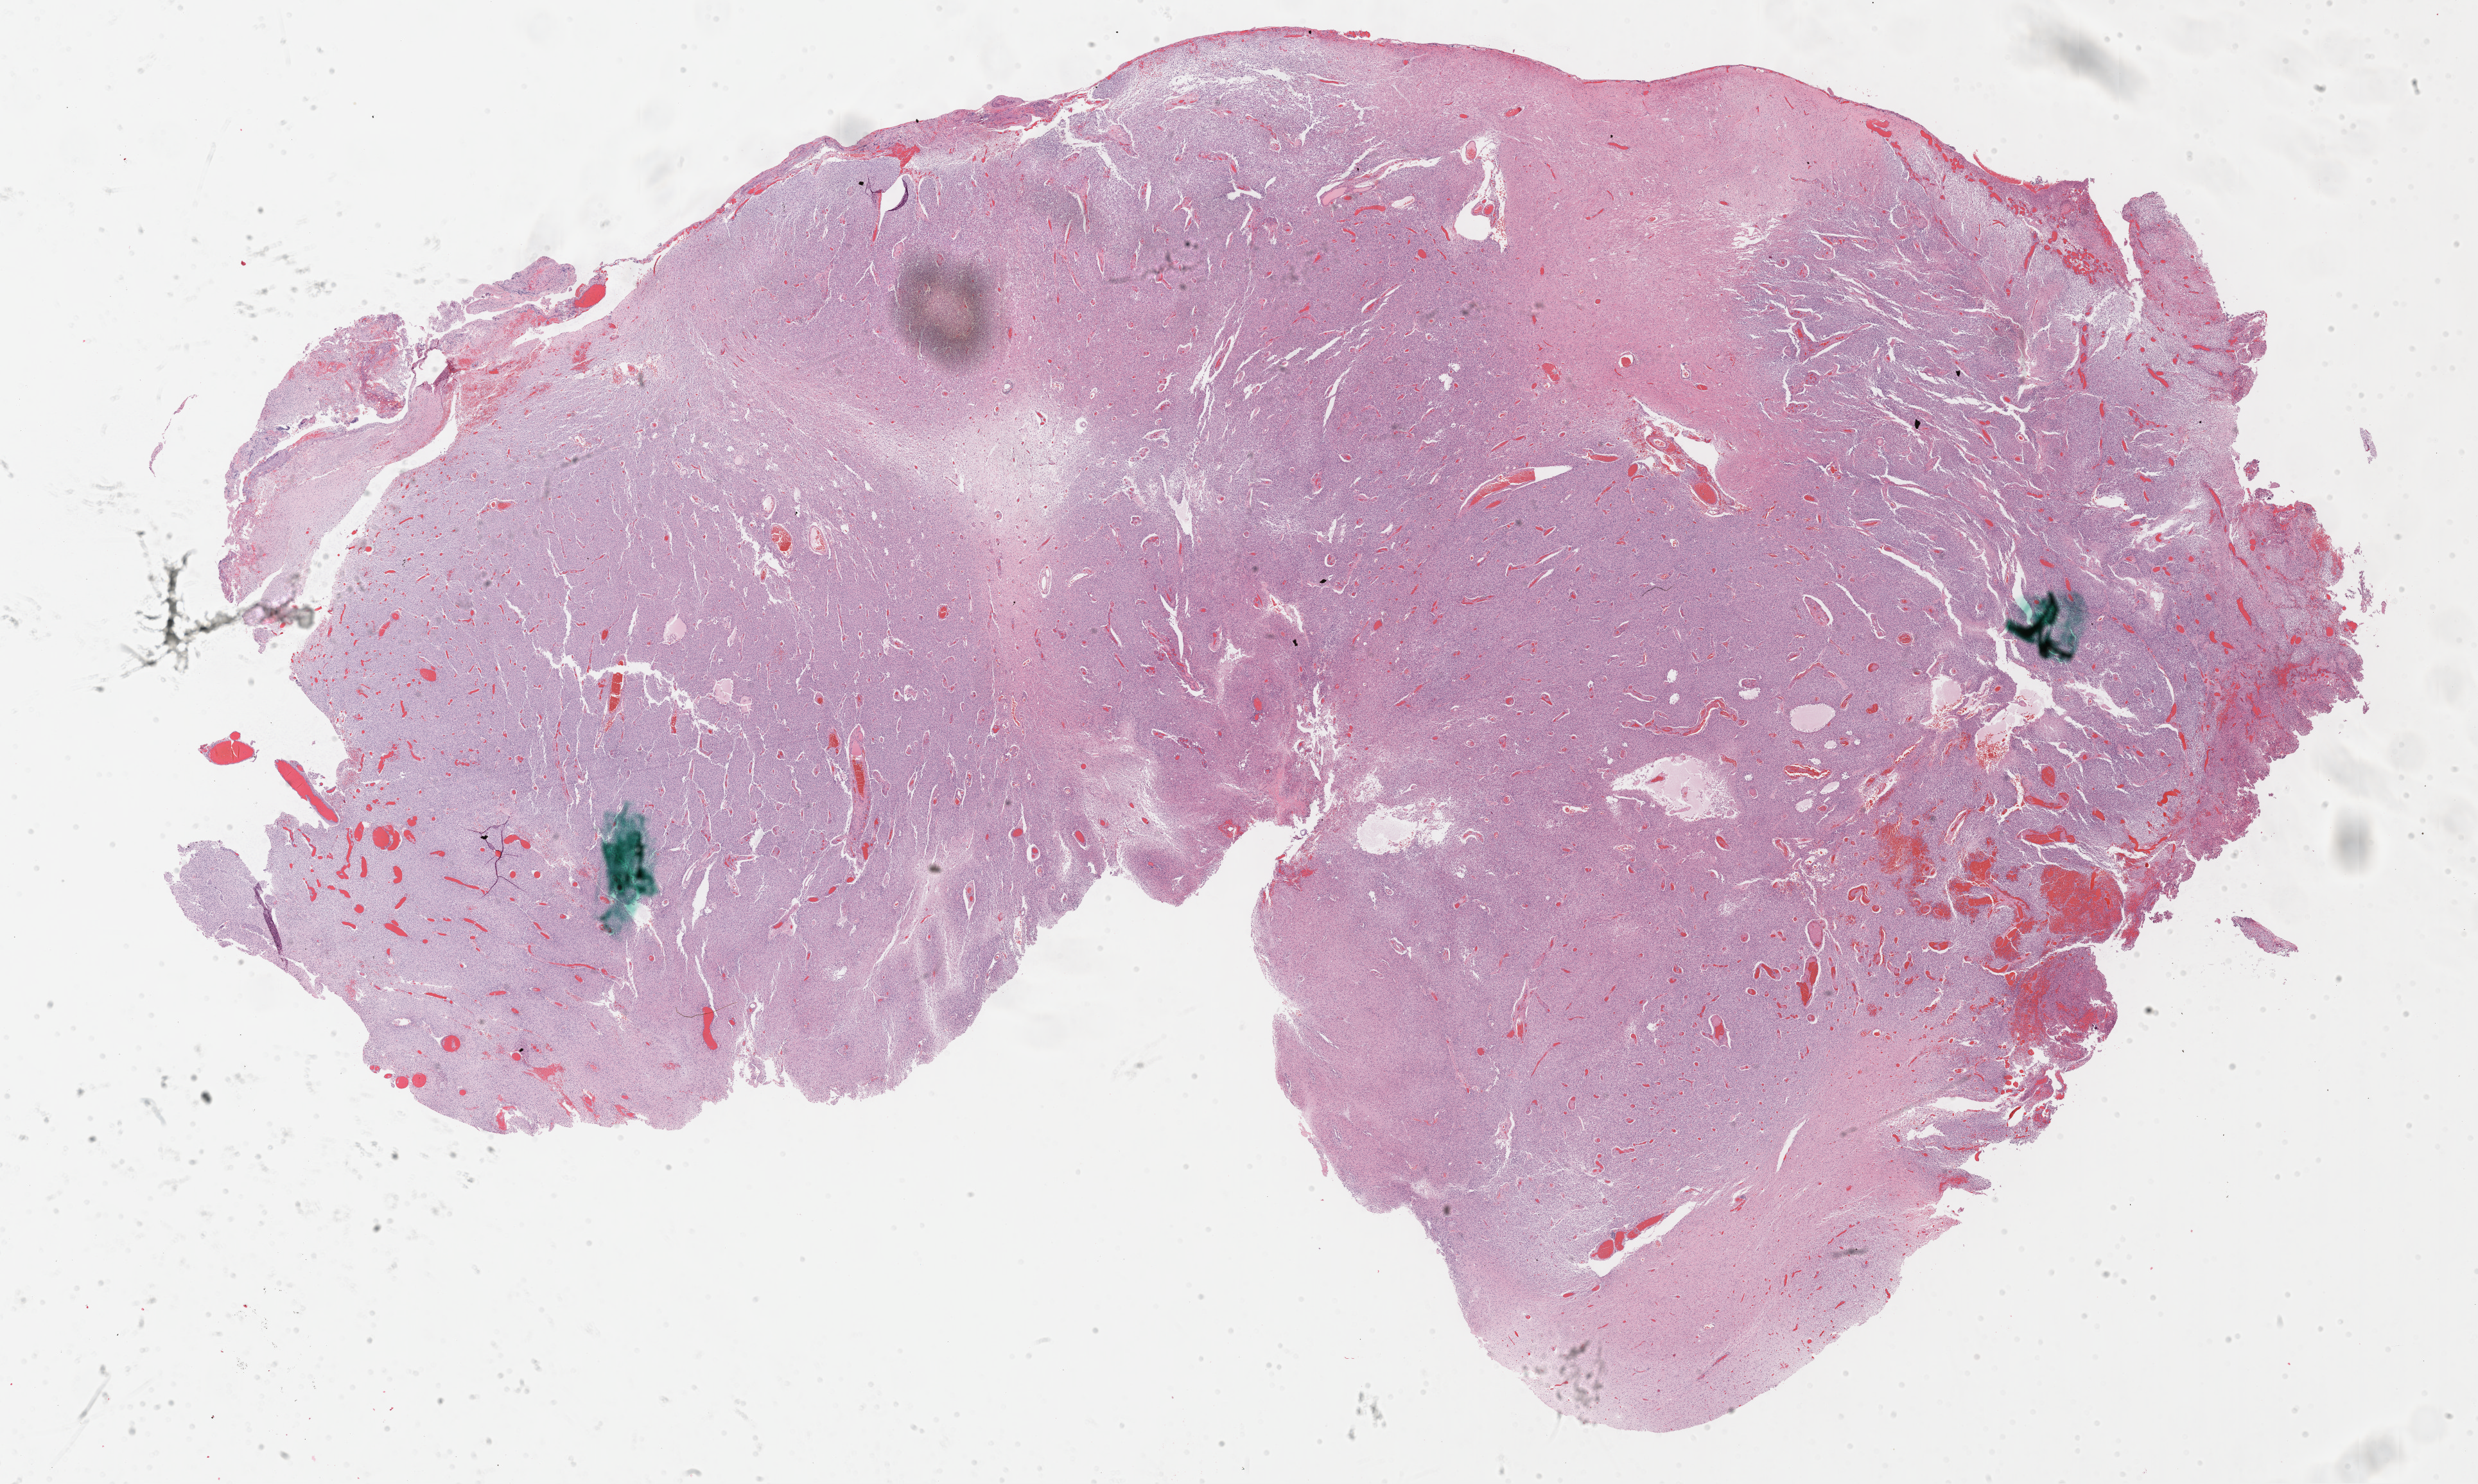
Digitized H&E-stained tissue section (whole slide) — low-resolution overview of the scanned area, about 31.2 x 18.7 mm. Formalin-fixed paraffin-embedded (FFPE) diagnostic section. Sample: primary tumour, brain. Male, age 44 years at initial diagnosis. Histologic grade: G3 (poorly differentiated).
• diagnosis: Mixed glioma (cerebrum)
• laterality: left